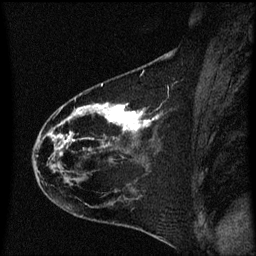
Breast MRI (dynamic contrast-enhanced), one sagittal slice. Slice 25 of 60 in the series (ordered by position). Dynamic contrast-enhanced series, image 2 of 3 at this slice position (ordered by acquisition). 1.5 T. TE 4.2 ms, TR 8.4 ms. 2 mm slice thickness. 256 × 256 image matrix, field of view 200 × 200 mm. Female patient, age 35 years. From the clinical record (not read from this slice): setting: breast cancer imaged before/during neoadjuvant chemotherapy; receptor status: HER2-positive.
Outlined on this slice (semi-automatic segmentation, software-assisted and operator-edited):
- analysis volume of interest (the breast-tissue region the enhancement analysis was run in; not a lesion): bounding box (x1, y1, x2, y2) in pixels: (32, 68, 174, 173)
- tumour enhancement mask (voxels above the 70 % enhancement threshold inside the analysis volume of interest): (50, 104, 159, 157)